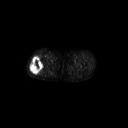
FDG PET of an extremity soft-tissue mass (from a PET/CT study), one axial slice. Slice 248 of 267 in the series (ordered by position). 3.27 mm slice thickness. 128 × 128 image matrix, field of view 700 × 700 mm. Patient: male, 43 years. Case-level facts recorded for this patient, not image findings: histological type: poorly differentiated synovial sarcoma; grade: high; site of the primary tumour: right buttock.
Structures marked on this image (expert contour drawn on MRI and transferred to this co-registered scan by the dataset authors):
- gross tumour volume including surrounding oedema: bounding box [x1, y1, x2, y2] px = [29, 57, 44, 75]
- gross tumour volume (mass): [29, 57, 43, 75]